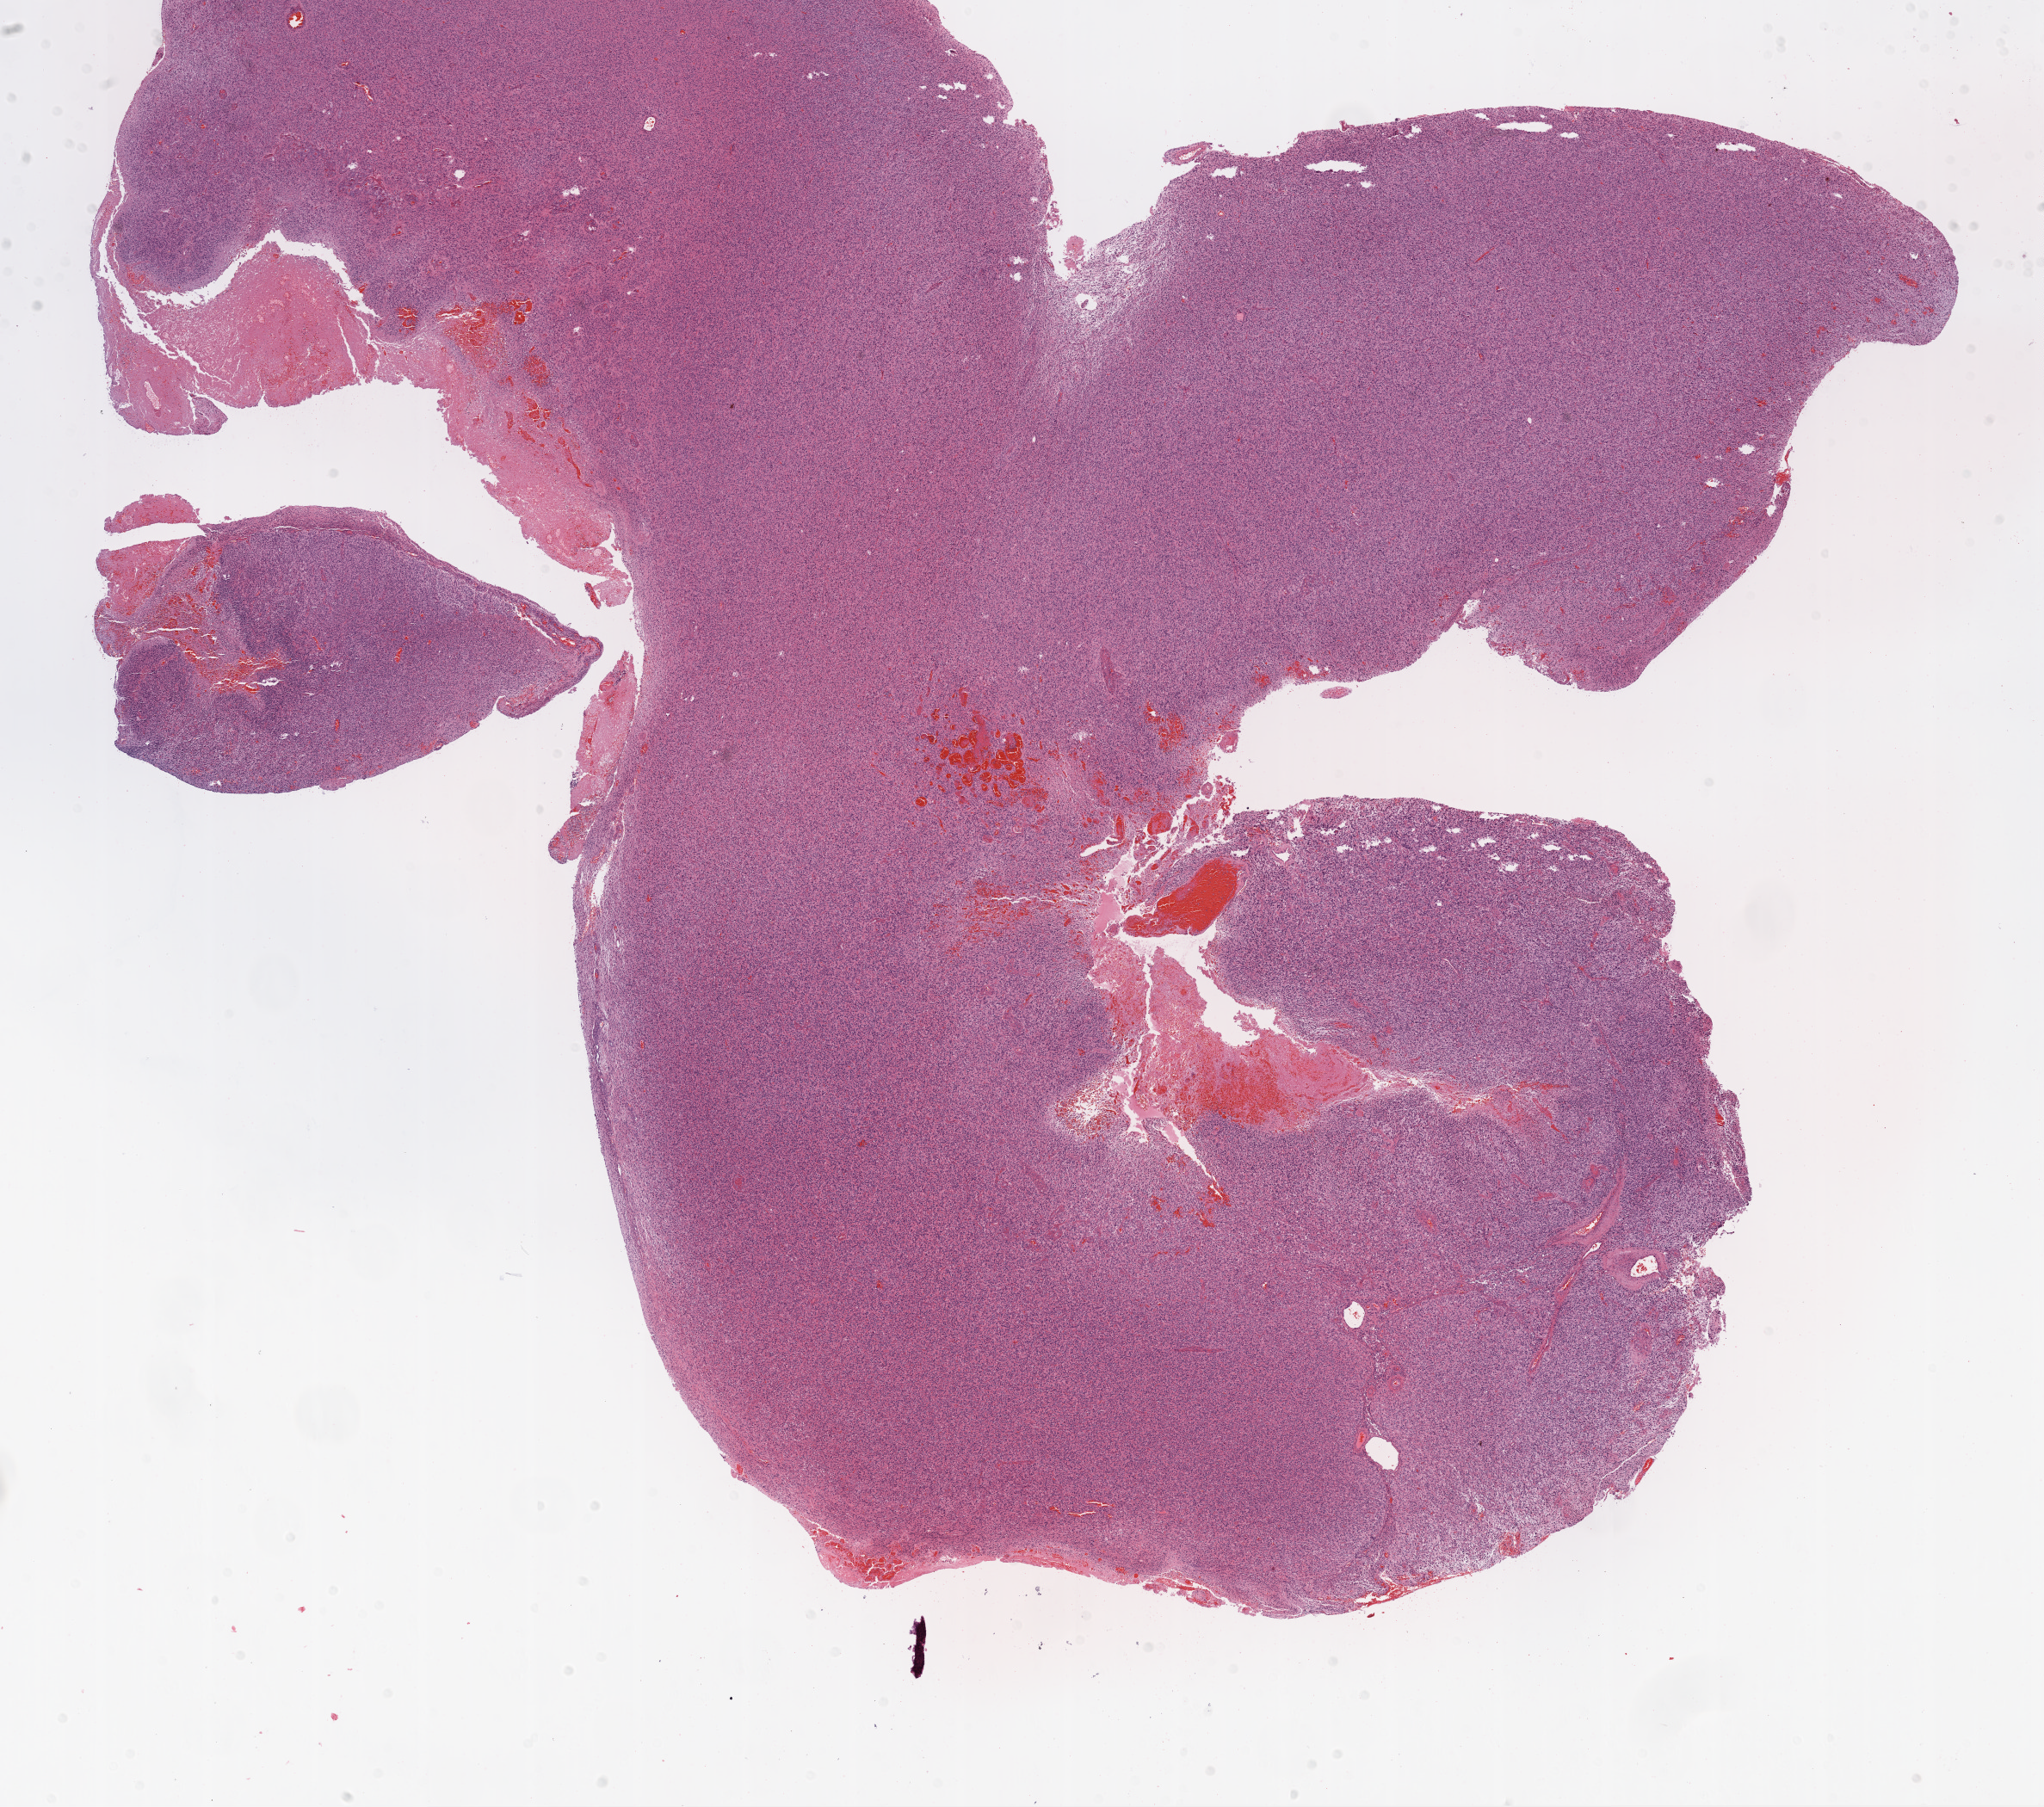
Whole-slide histology image, H&E — low-resolution overview of the scanned area, about 19.1 x 16.9 mm. Formalin-fixed paraffin-embedded (FFPE) diagnostic section. Brain, primary tumour sample. Patient: male, age at initial diagnosis 54 years.
Histologic diagnosis: Glioblastoma.